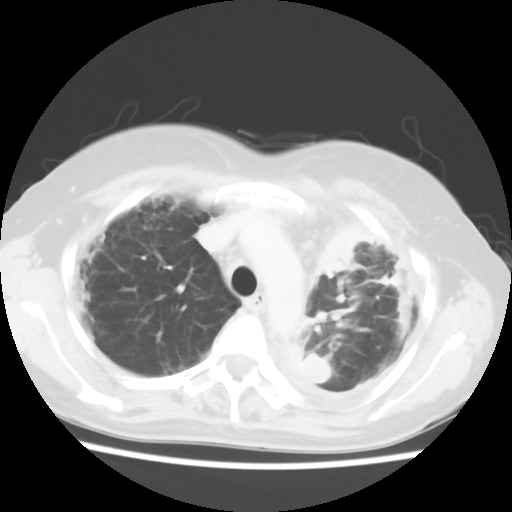
Chest CT, one axial slice. Slice 42 of 56 in the series (ordered by position). Reconstruction kernel STANDARD. 120 kVp. Lung window (W 1500 / L -600 HU). 5 mm slice thickness. 512 × 512 image matrix, field of view 309 × 309 mm. Female patient, age 56 years. Case-level facts recorded for this patient, not image findings: clinical TNM (as recorded): T1c N0 M1.
Structures marked on this image (rectangle marked by the reading radiologist):
- lung tumour (recorded histology: adenocarcinoma): bounding box [x1, y1, x2, y2] px = [300, 215, 365, 283]